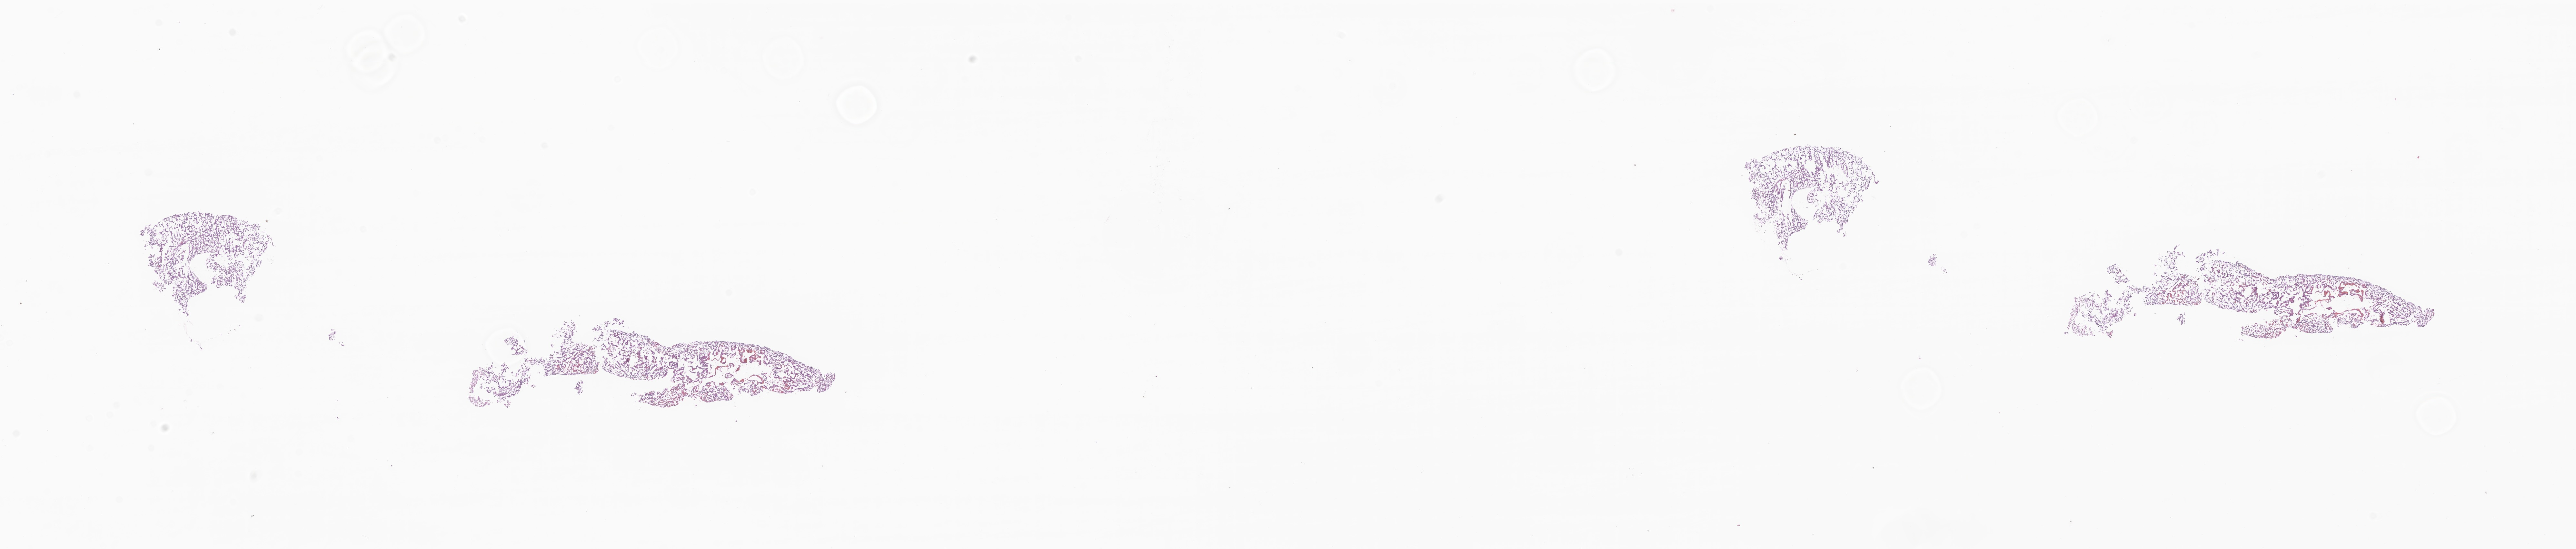
Digitized hematoxylin and eosin (H&E)-stained section of tumor tissue from the brain, a low-resolution overview of the entire scanned area, about 33.7 x 7.2 mm; cryosection (OCT / tissue freezing medium). Female patient, age 82 days.
Diagnosis: Neoplasm, malignant.